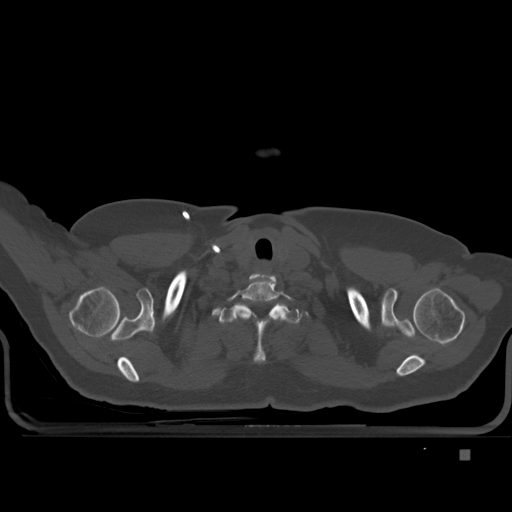
CT including the spine, one axial slice. Position 407 of 477 along the scan axis. Bone window (W 1800 / L 400 HU). 512 × 512 image matrix, field of view 422 × 422 mm. Patient: female, 74 years. From the clinical record (not read from this slice): primary cancer: colon.
Annotated regions visible in this slice (semi-automatically segmented with operator editing):
- T1 vertebra: bounding box <233,304,288,363> (left, top, right, bottom; pixels)